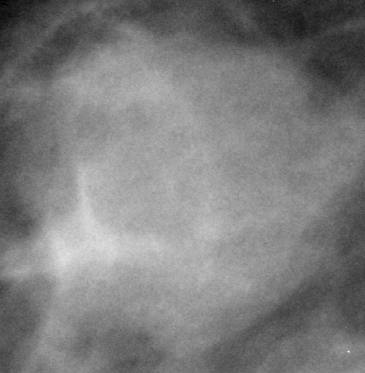
Crop from a digitized film mammogram around one marked abnormality, right breast, MLO view, BI-RADS breast density category 2 (scale 1–4).
- Mass, shape round, margins microlobulated; BI-RADS assessment category 4; pathology result (as recorded, not read from the image): benign.